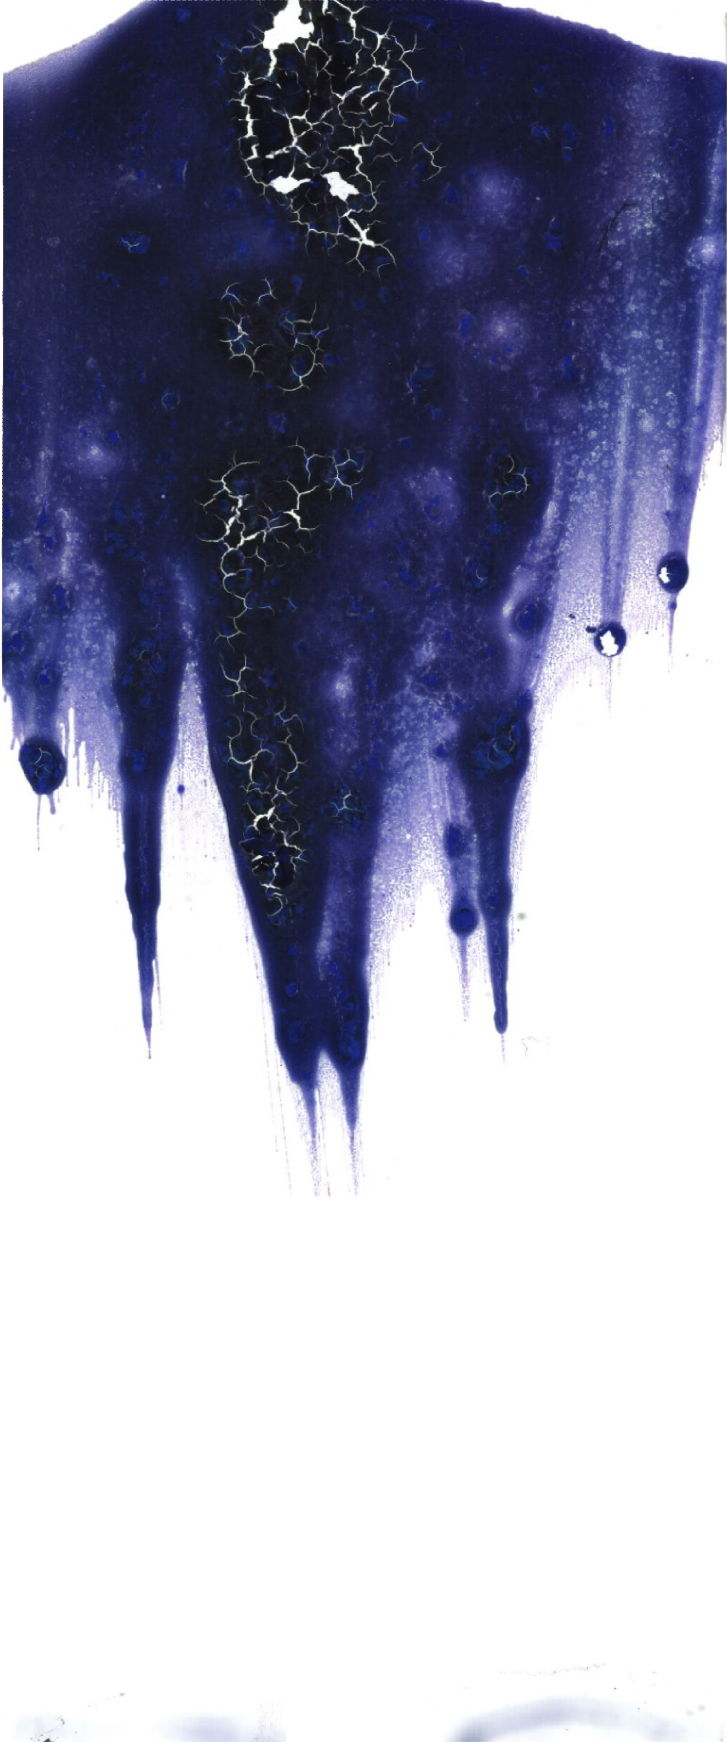
Whole-slide image of a May-Grünwald-Giemsa (MGG)-stained bone marrow aspirate smear — a low-resolution overview of the entire scanned area, about 20.6 x 49.4 mm. Female patient.
Diagnosis: Chronic Phase Chronic Myeloid Leukemia, BCR-ABL1 Positive.